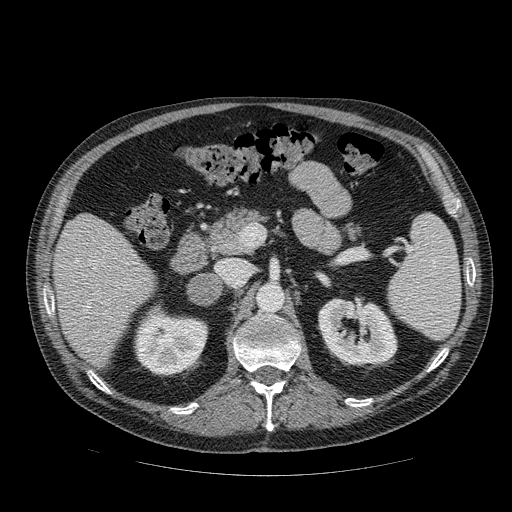
Contrast-enhanced abdominal CT, one axial slice; position 47 of 111 along the scan axis; 120 kVp; intravenous contrast given; soft-tissue window (W 400 / L 40 HU); 512 × 512 image matrix, field of view 420 × 420 mm. Patient: male, 56 years. Case-level facts recorded for this patient, not image findings: diagnosis: adrenocortical carcinoma; tumour side: right adrenal; tumour size at pathology: 9 cm; Ki-67 index: 48 %.
Outlined on this slice (semi-automatically segmented with operator editing):
- mass: box from (x=190, y=276) to (x=220, y=304) px